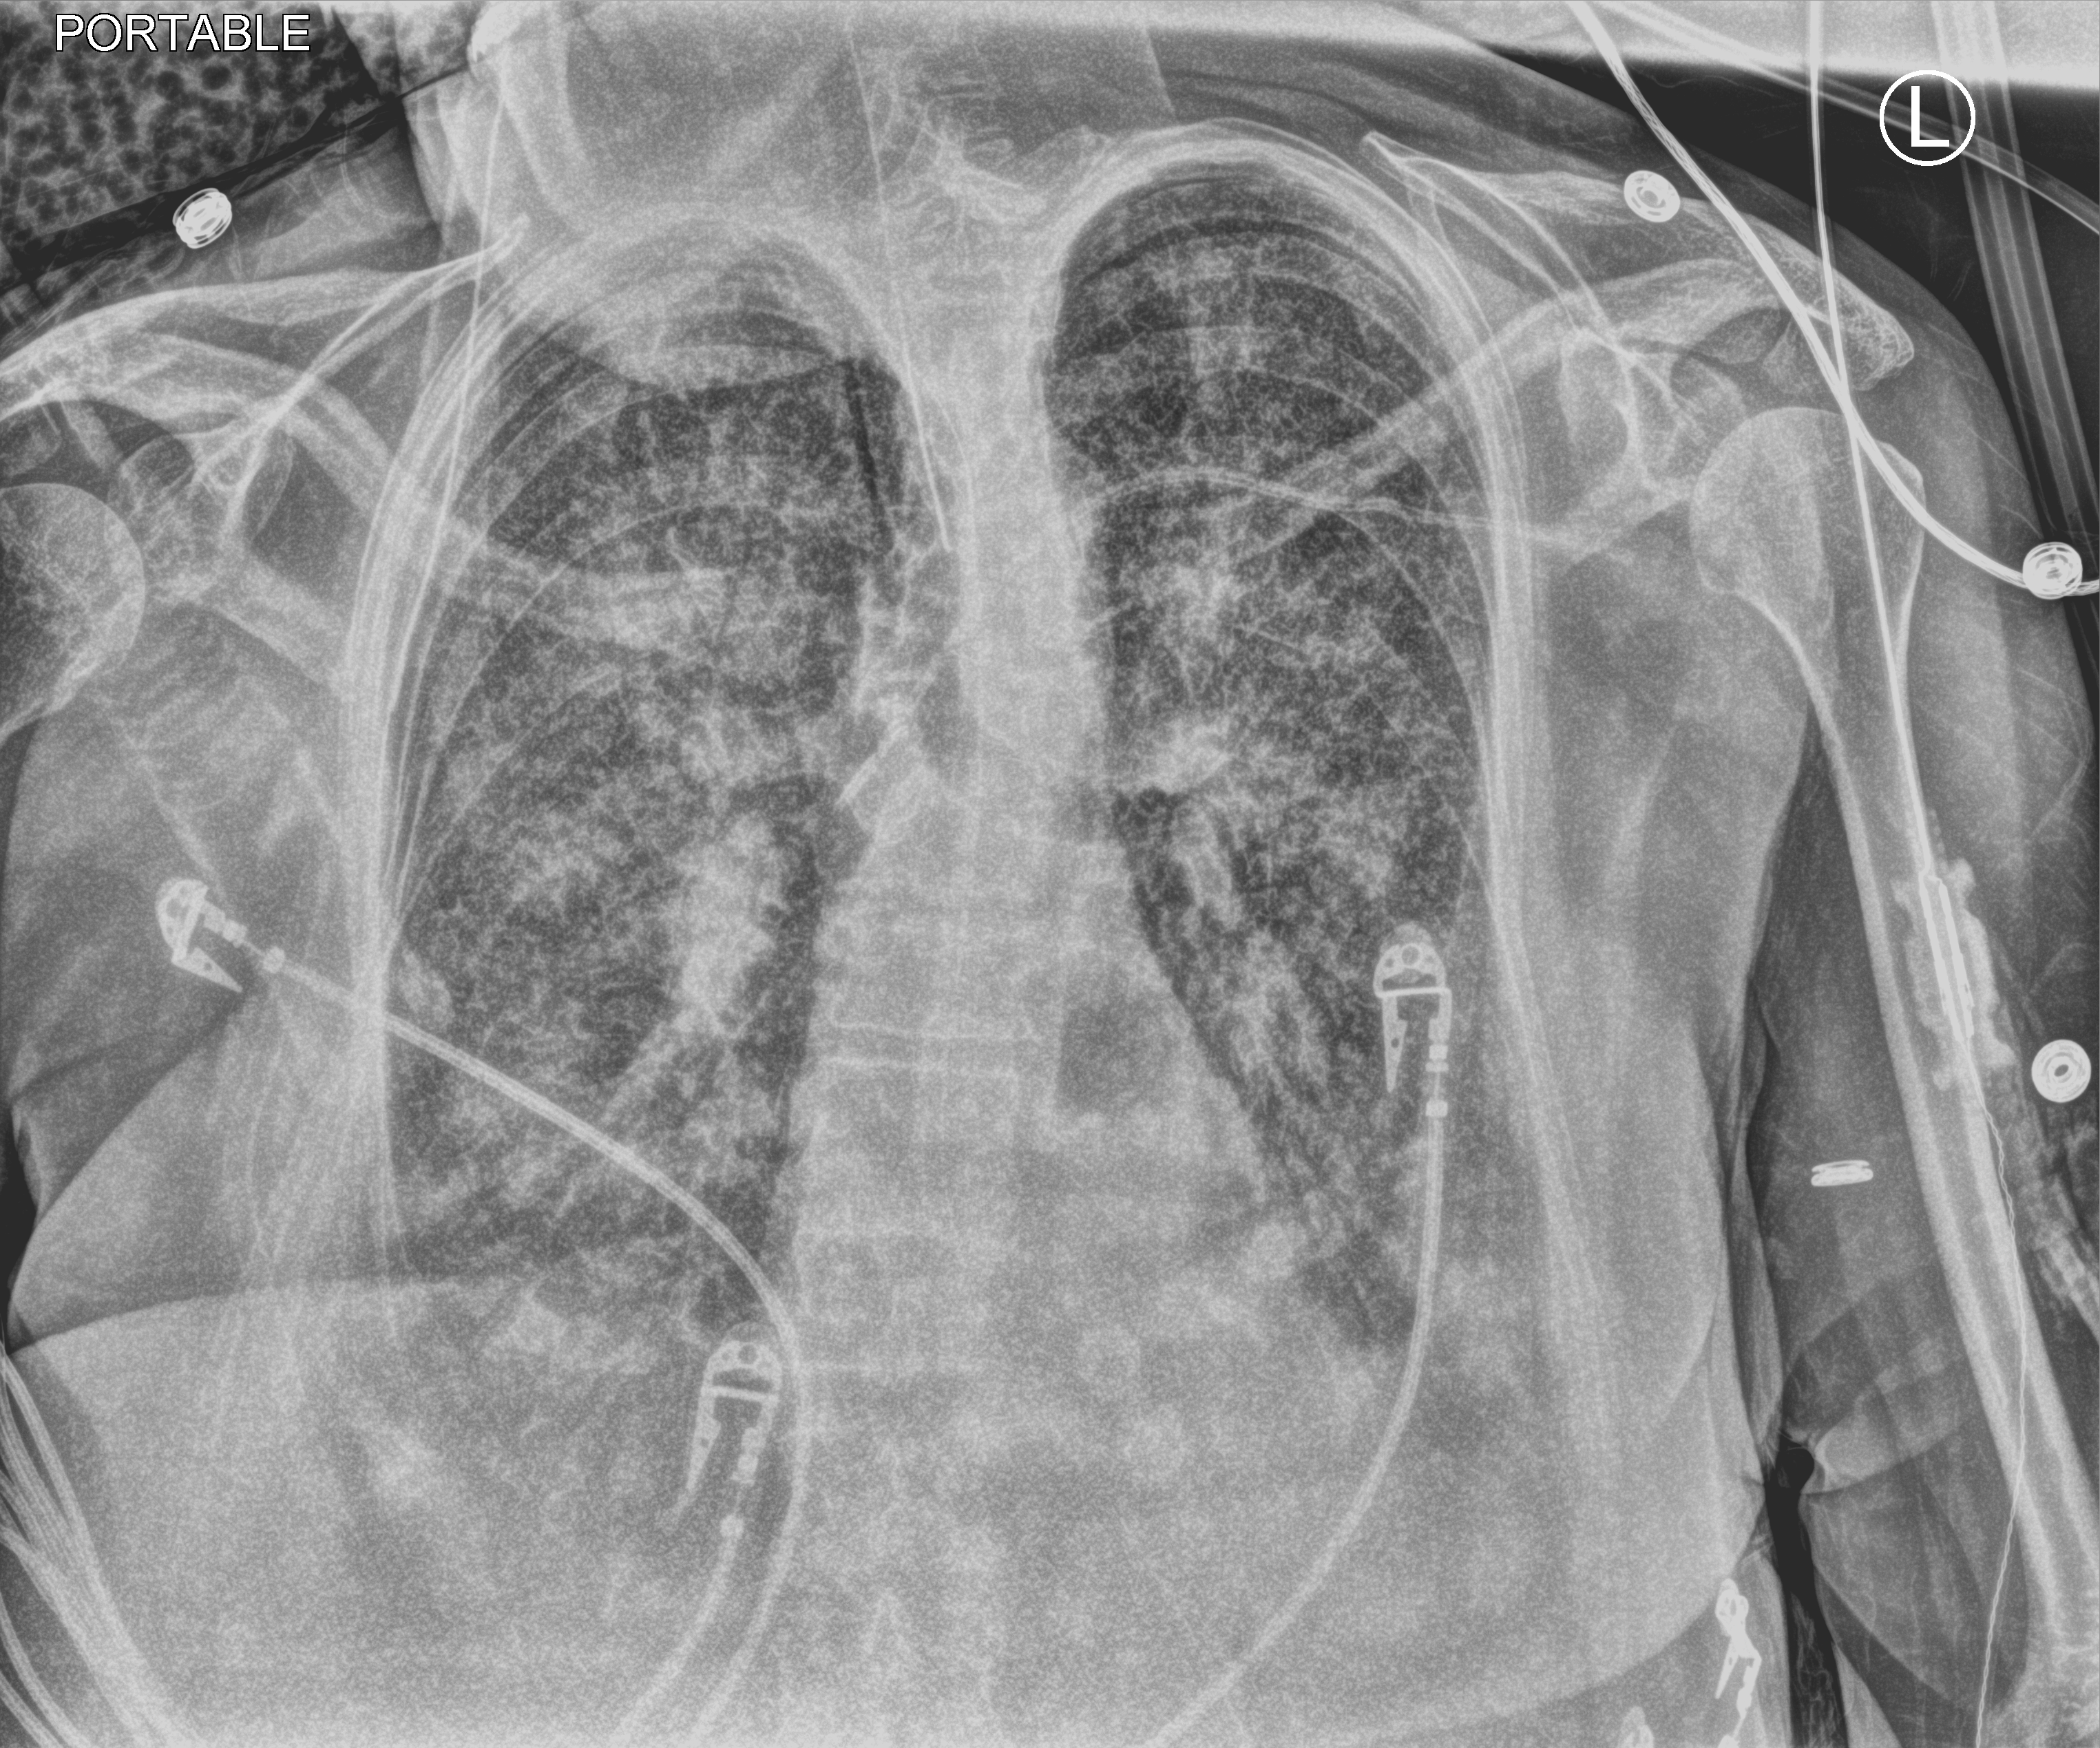
Bedside chest radiograph (computed radiography); anteroposterior (AP) projection. Female patient hospitalised with COVID-19, age 75–90 years.
Hospital-stay facts (about this admission, not read from this image; timing relative to this image not recorded):
- mechanically ventilated during this hospital stay: yes
- admitted to intensive care during this hospital stay: yes
- COPD (admission record): no